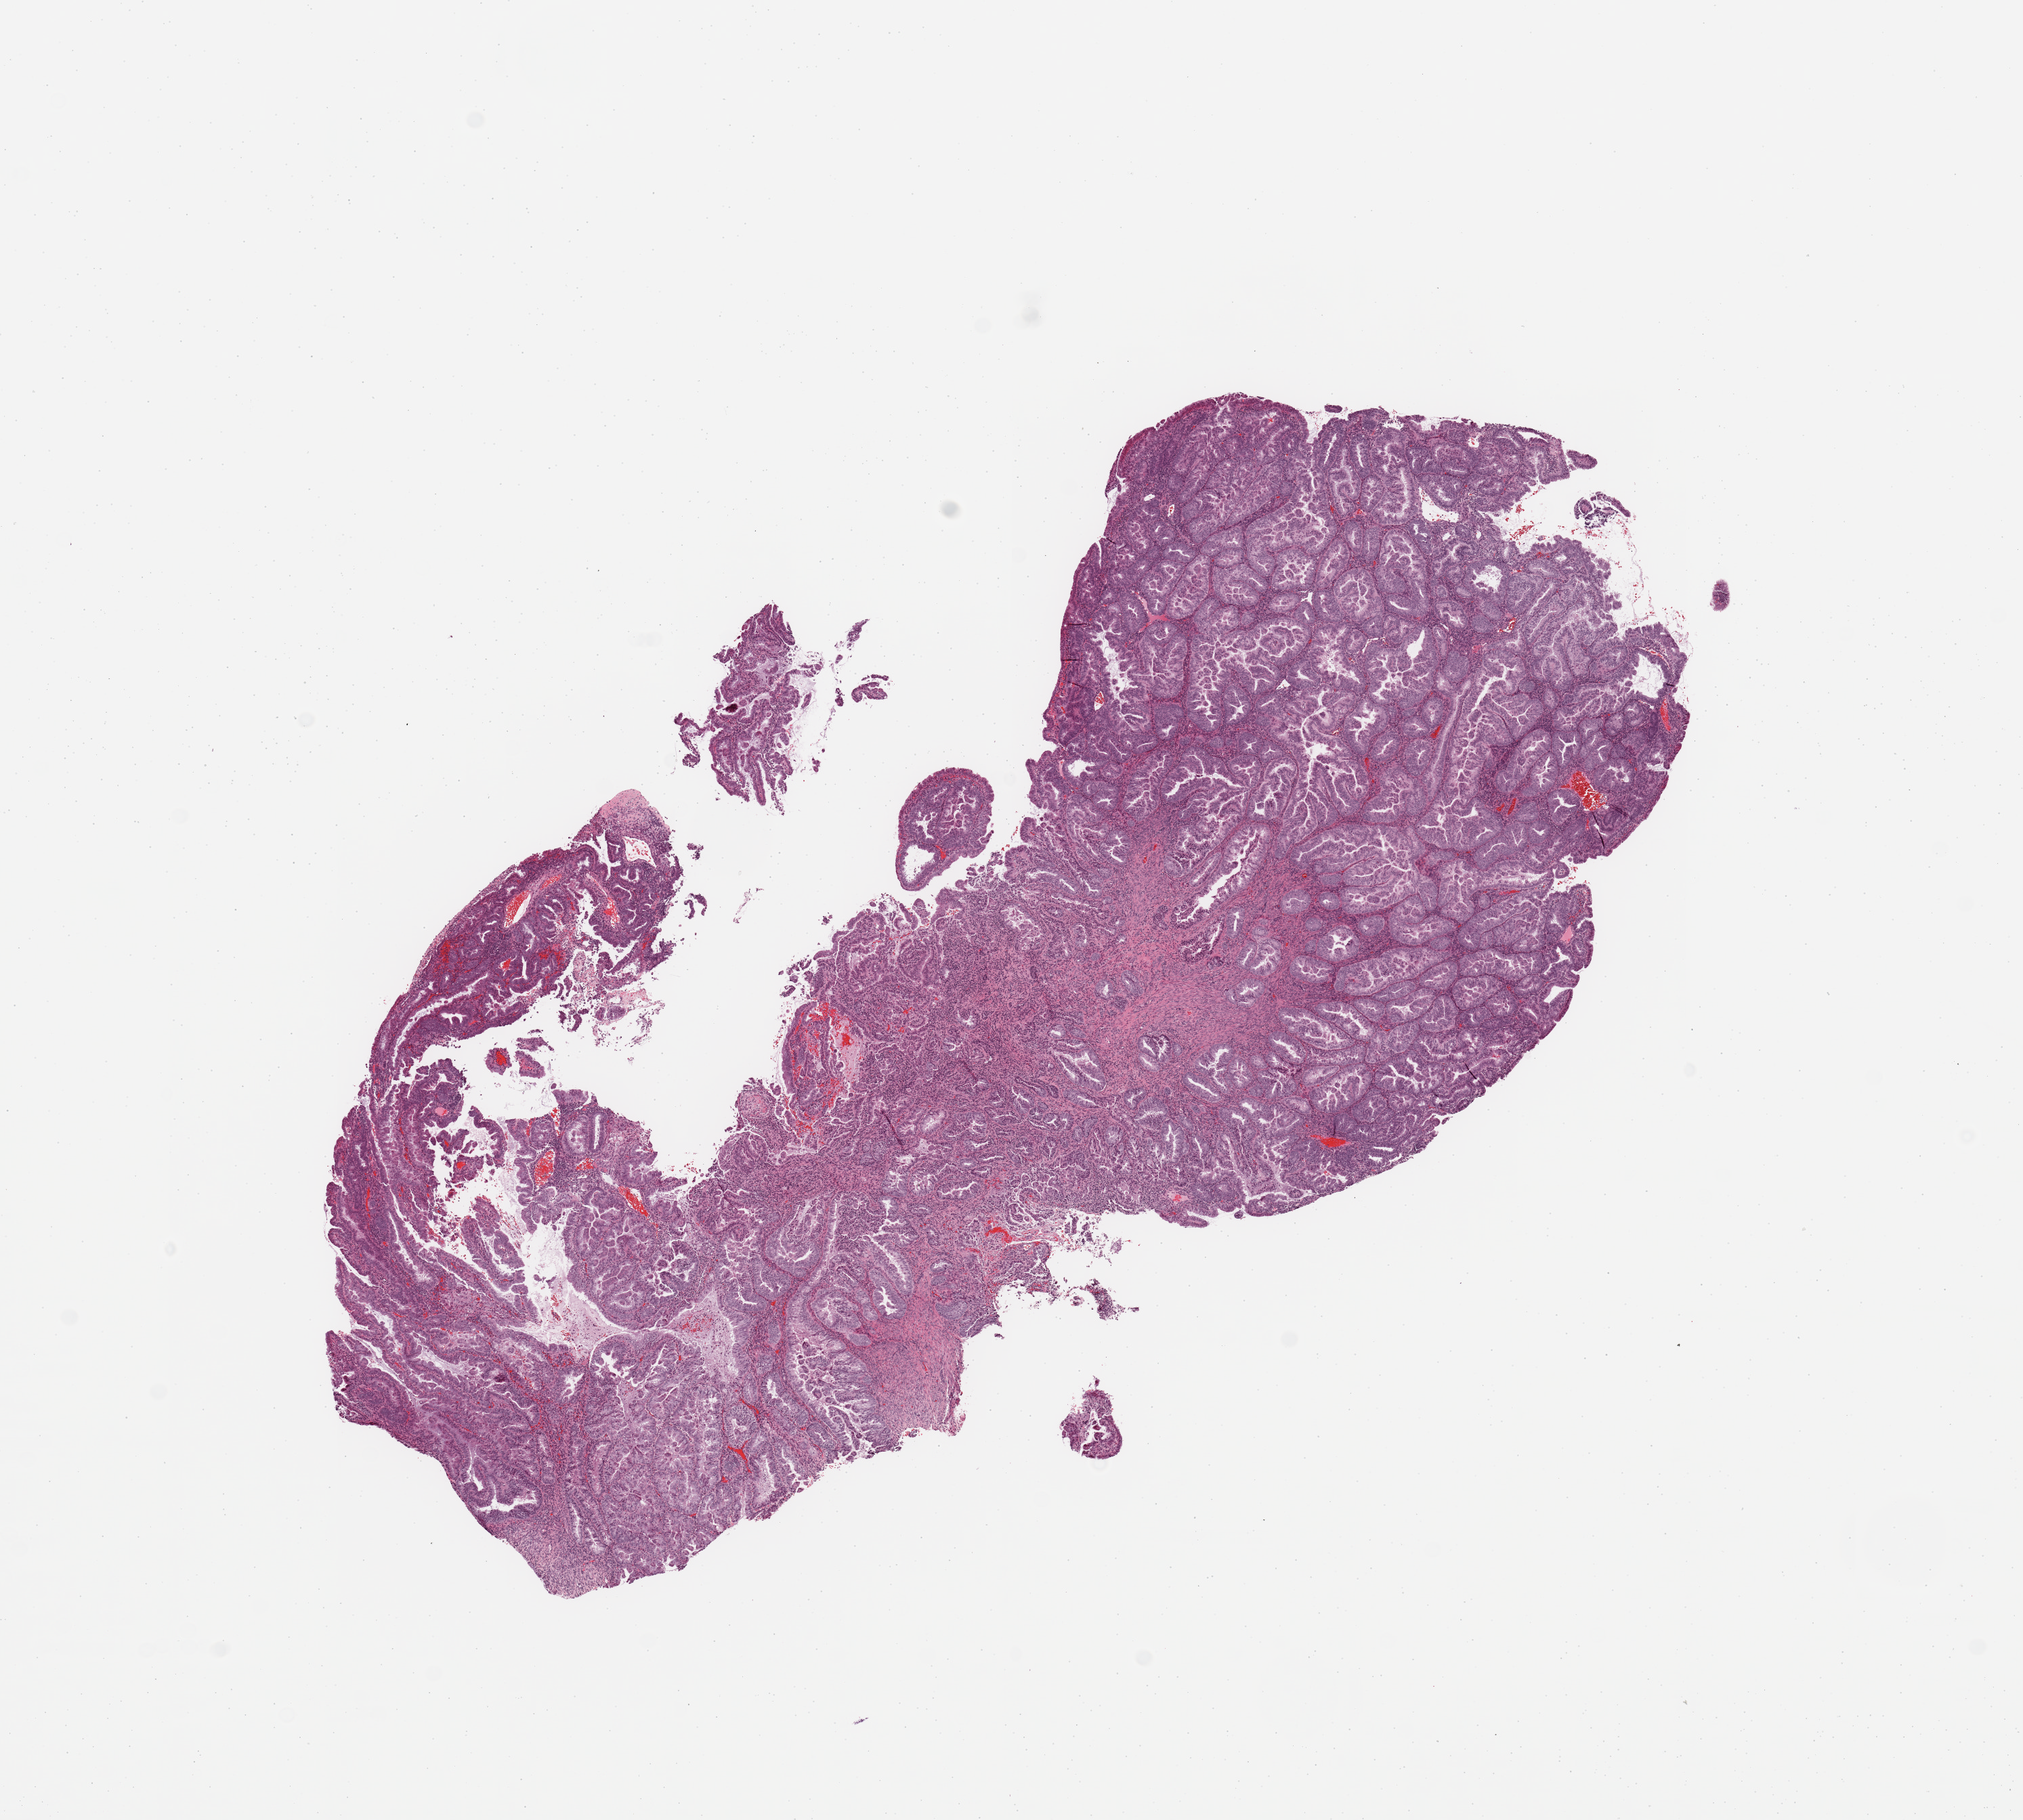
Whole-slide histology image, H&E-stained — whole scanned area (about 11.8 x 10.6 mm, from a 20x scan) shown as a low-resolution overview. Tumour tissue sample, sampled site: uterus. 60-year-old female patient. Histologic grade: G1 (well differentiated). Pathologist review of this section (percent, as recorded): tumour nuclei 90%, necrosis 1%.
• AJCC pathologic stage: I
• diagnosis: Endometrioid adenocarcinoma, NOS